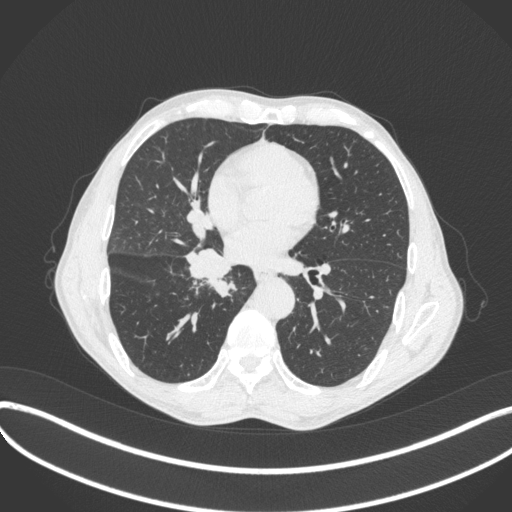
Chest CT, one axial slice. Slice 200 of 481 in the series (ordered by position). Reconstruction kernel B31f. 120 kVp. Lung window (W 1500 / L -600 HU). 1 mm slice thickness. 512 × 512 image matrix, field of view 400 × 400 mm. Male patient, age 65 years. Case-level facts recorded for this patient, not image findings: clinical TNM (as recorded): T2a N0 M0.
Structures marked on this image (bounding box drawn by a radiologist):
- lung tumour (recorded histology: squamous cell carcinoma): bounding box <182,245,242,295> (left, top, right, bottom; pixels)